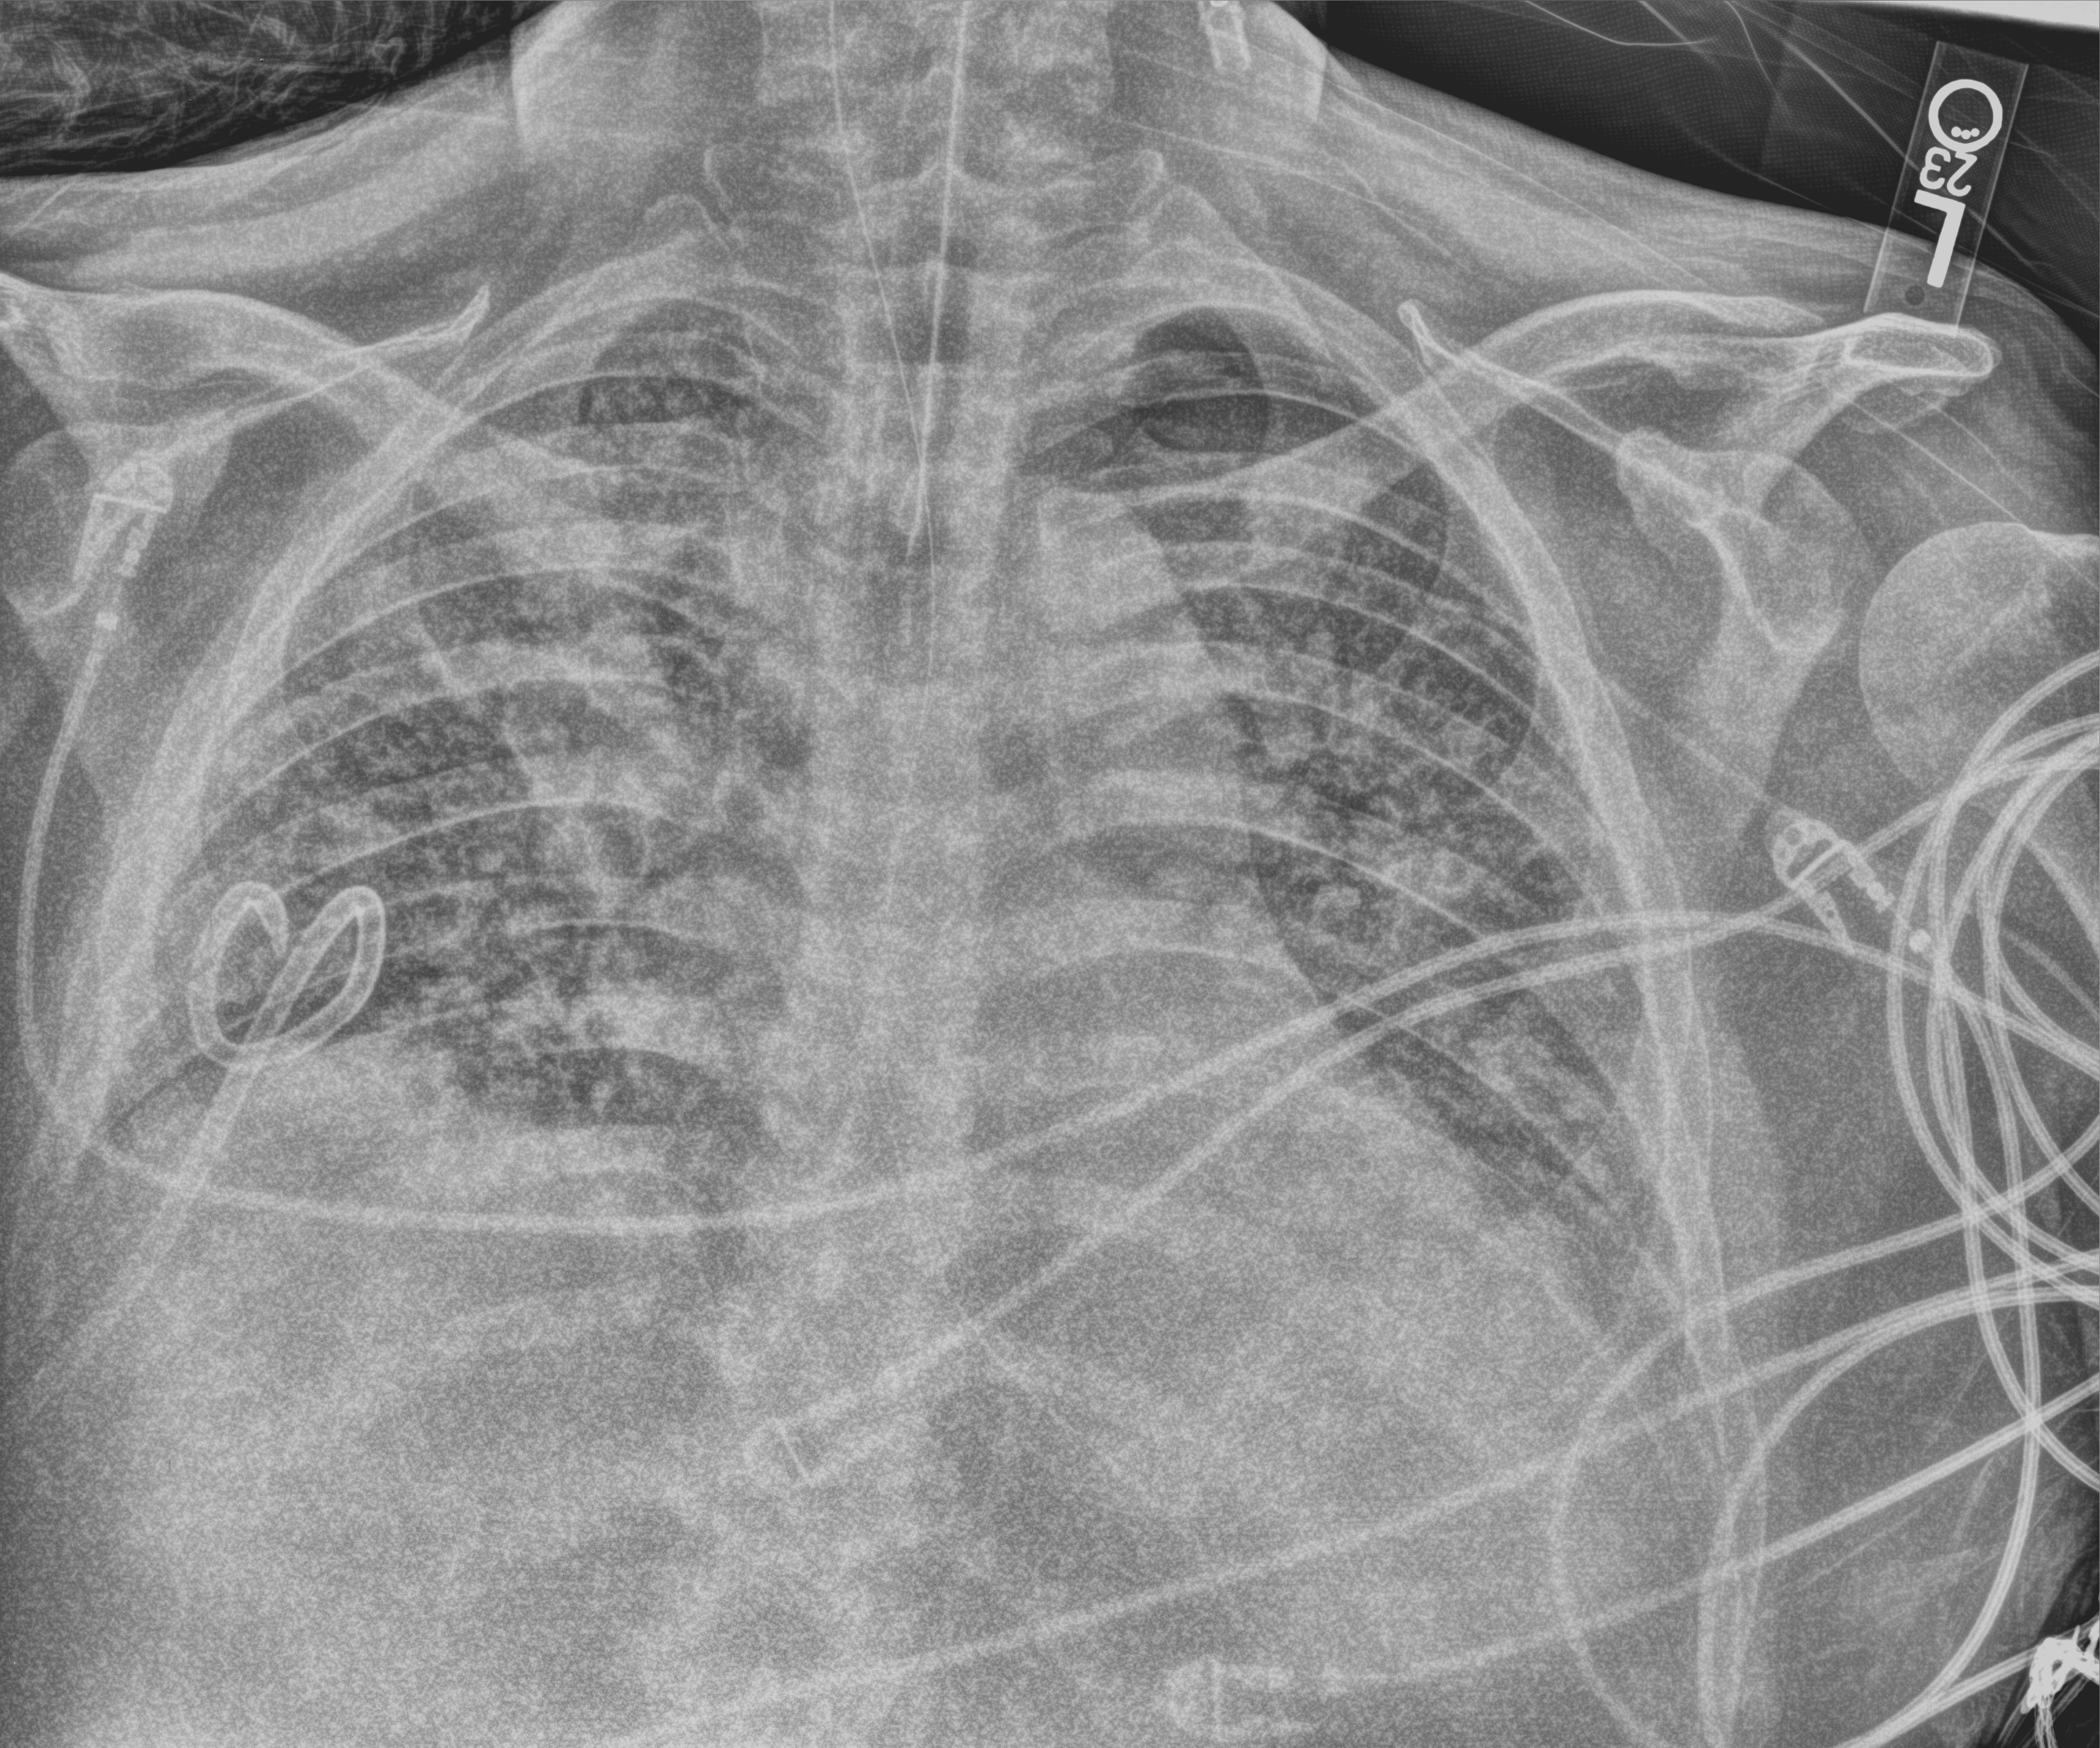
Portable chest radiograph; anteroposterior (AP) projection. Adult patient hospitalised with COVID-19, age 18–59 years.
Hospital-stay facts (about this admission, not read from this image; timing relative to this image not recorded):
- mechanically ventilated during this hospital stay: yes
- length of hospital stay: 31 days